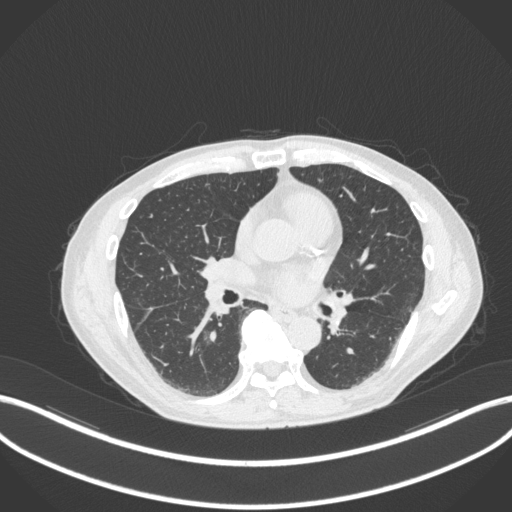
Chest CT, one axial slice. Position 160 of 324 along the scan axis. Lung window (W 1500 / L -600 HU). 1 mm slice thickness. 512 × 512 image matrix. Patient: male, 61 years. From the clinical record (not read from this slice): clinical TNM (as recorded): T1c N0 M0.
Structures marked on this image (rectangle marked by the reading radiologist):
- lung tumour (recorded histology: adenocarcinoma): bounding box <198,325,219,350> (left, top, right, bottom; pixels)